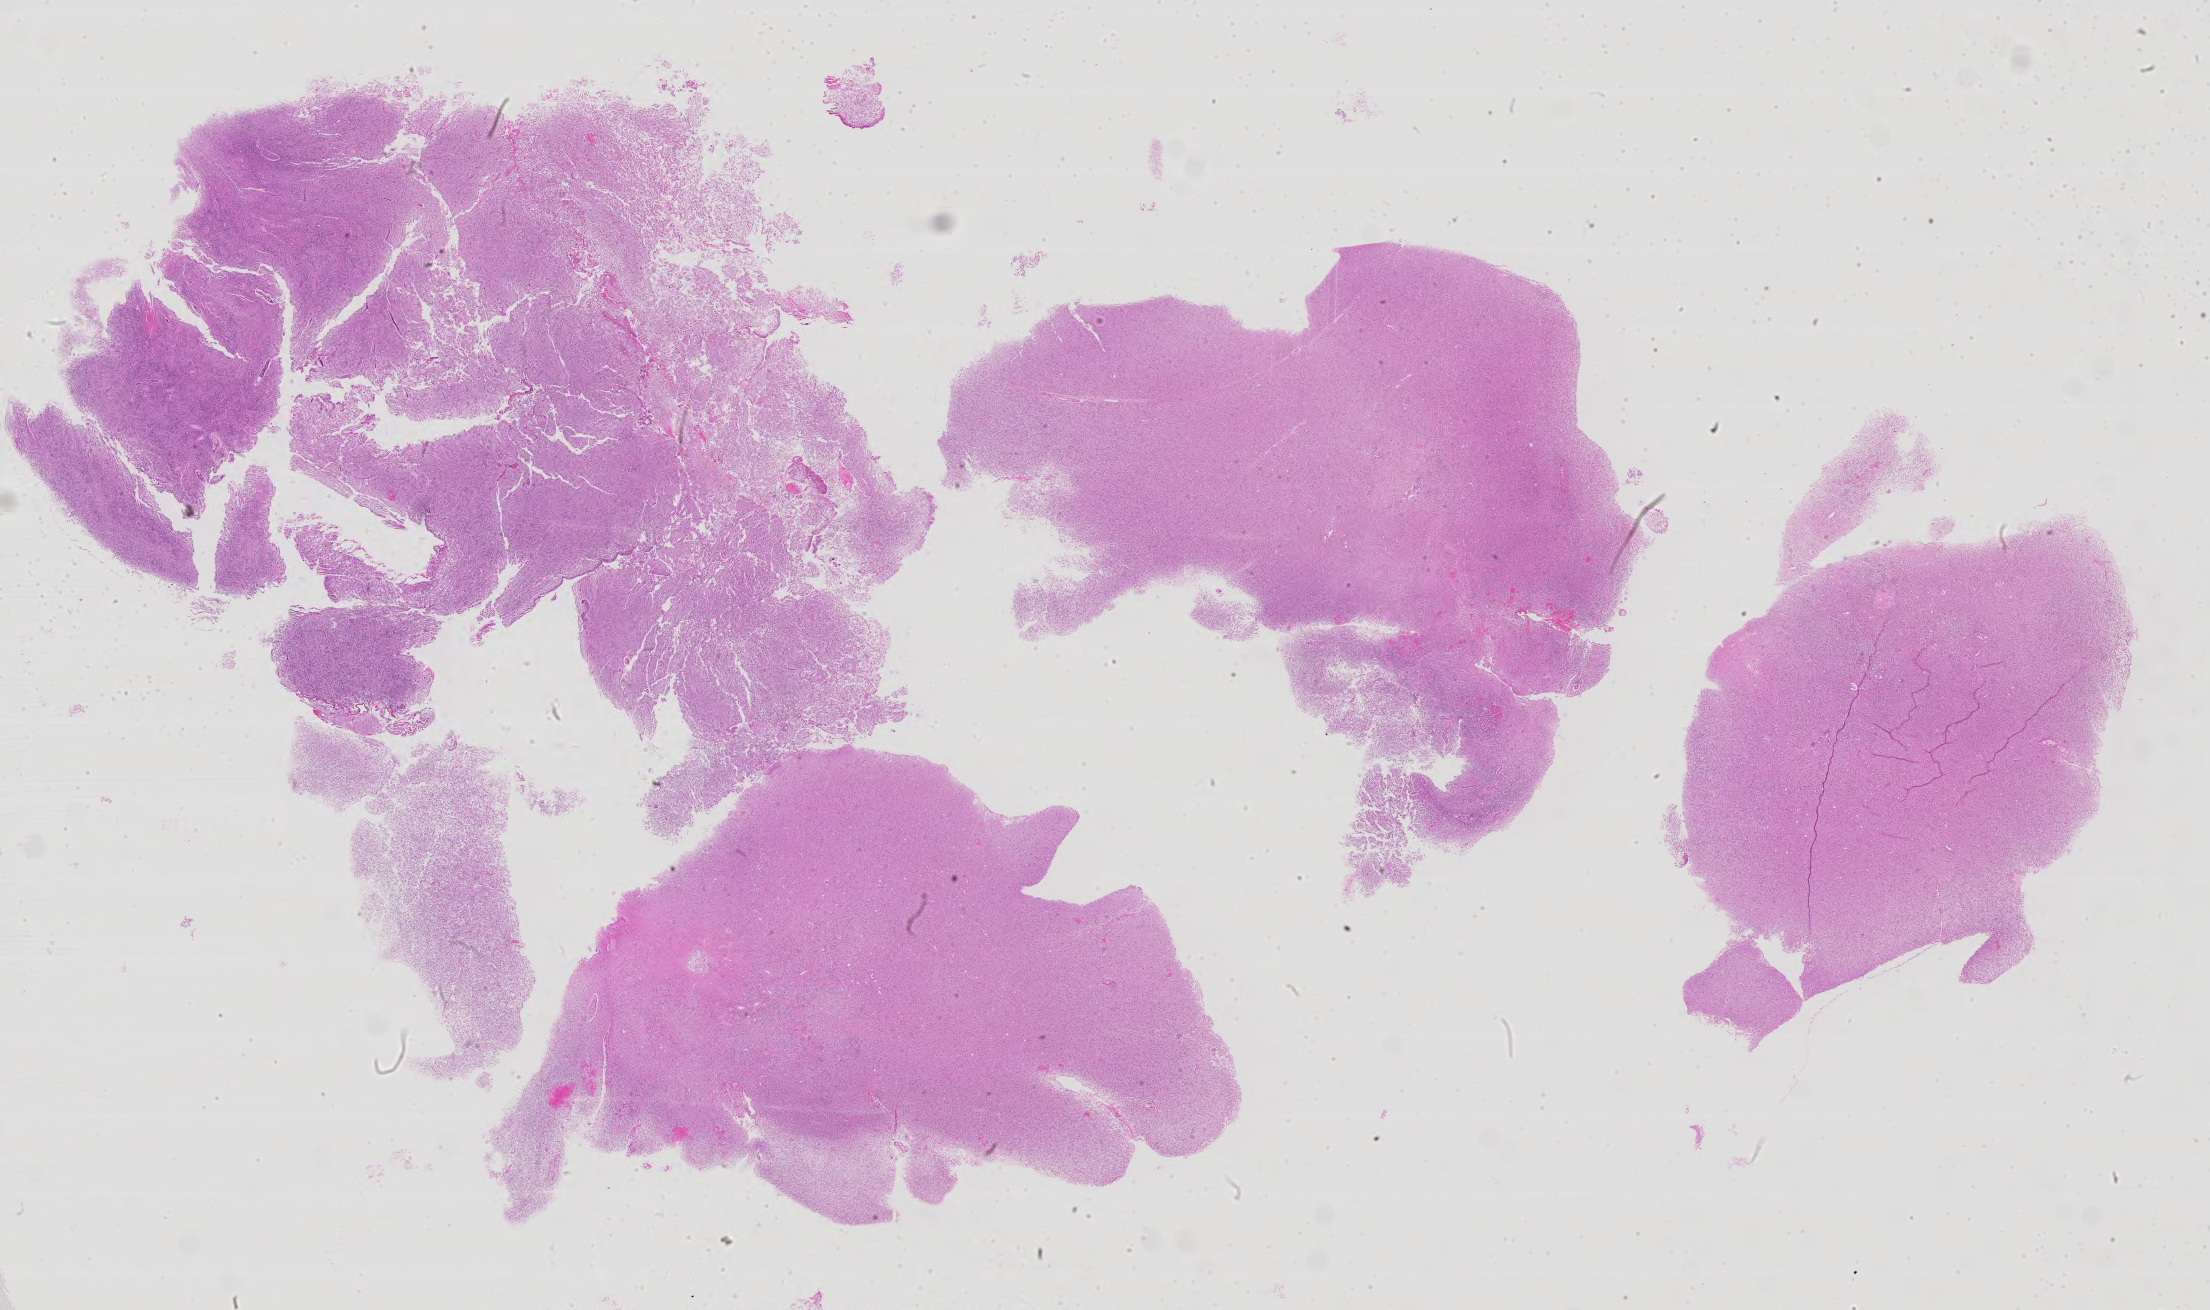
Digitized Hematoxylin and eosin (H&E) stained tissue section (whole slide) — low-resolution overview of the scanned area, about 35.4 x 21.0 mm (from a 40x scan); FFPE section; brain, primary tumour sample. Male patient; age at initial diagnosis 42 years. Histologic grade: G3 (poorly differentiated).
* pathologic diagnosis: Mixed glioma (cerebrum)